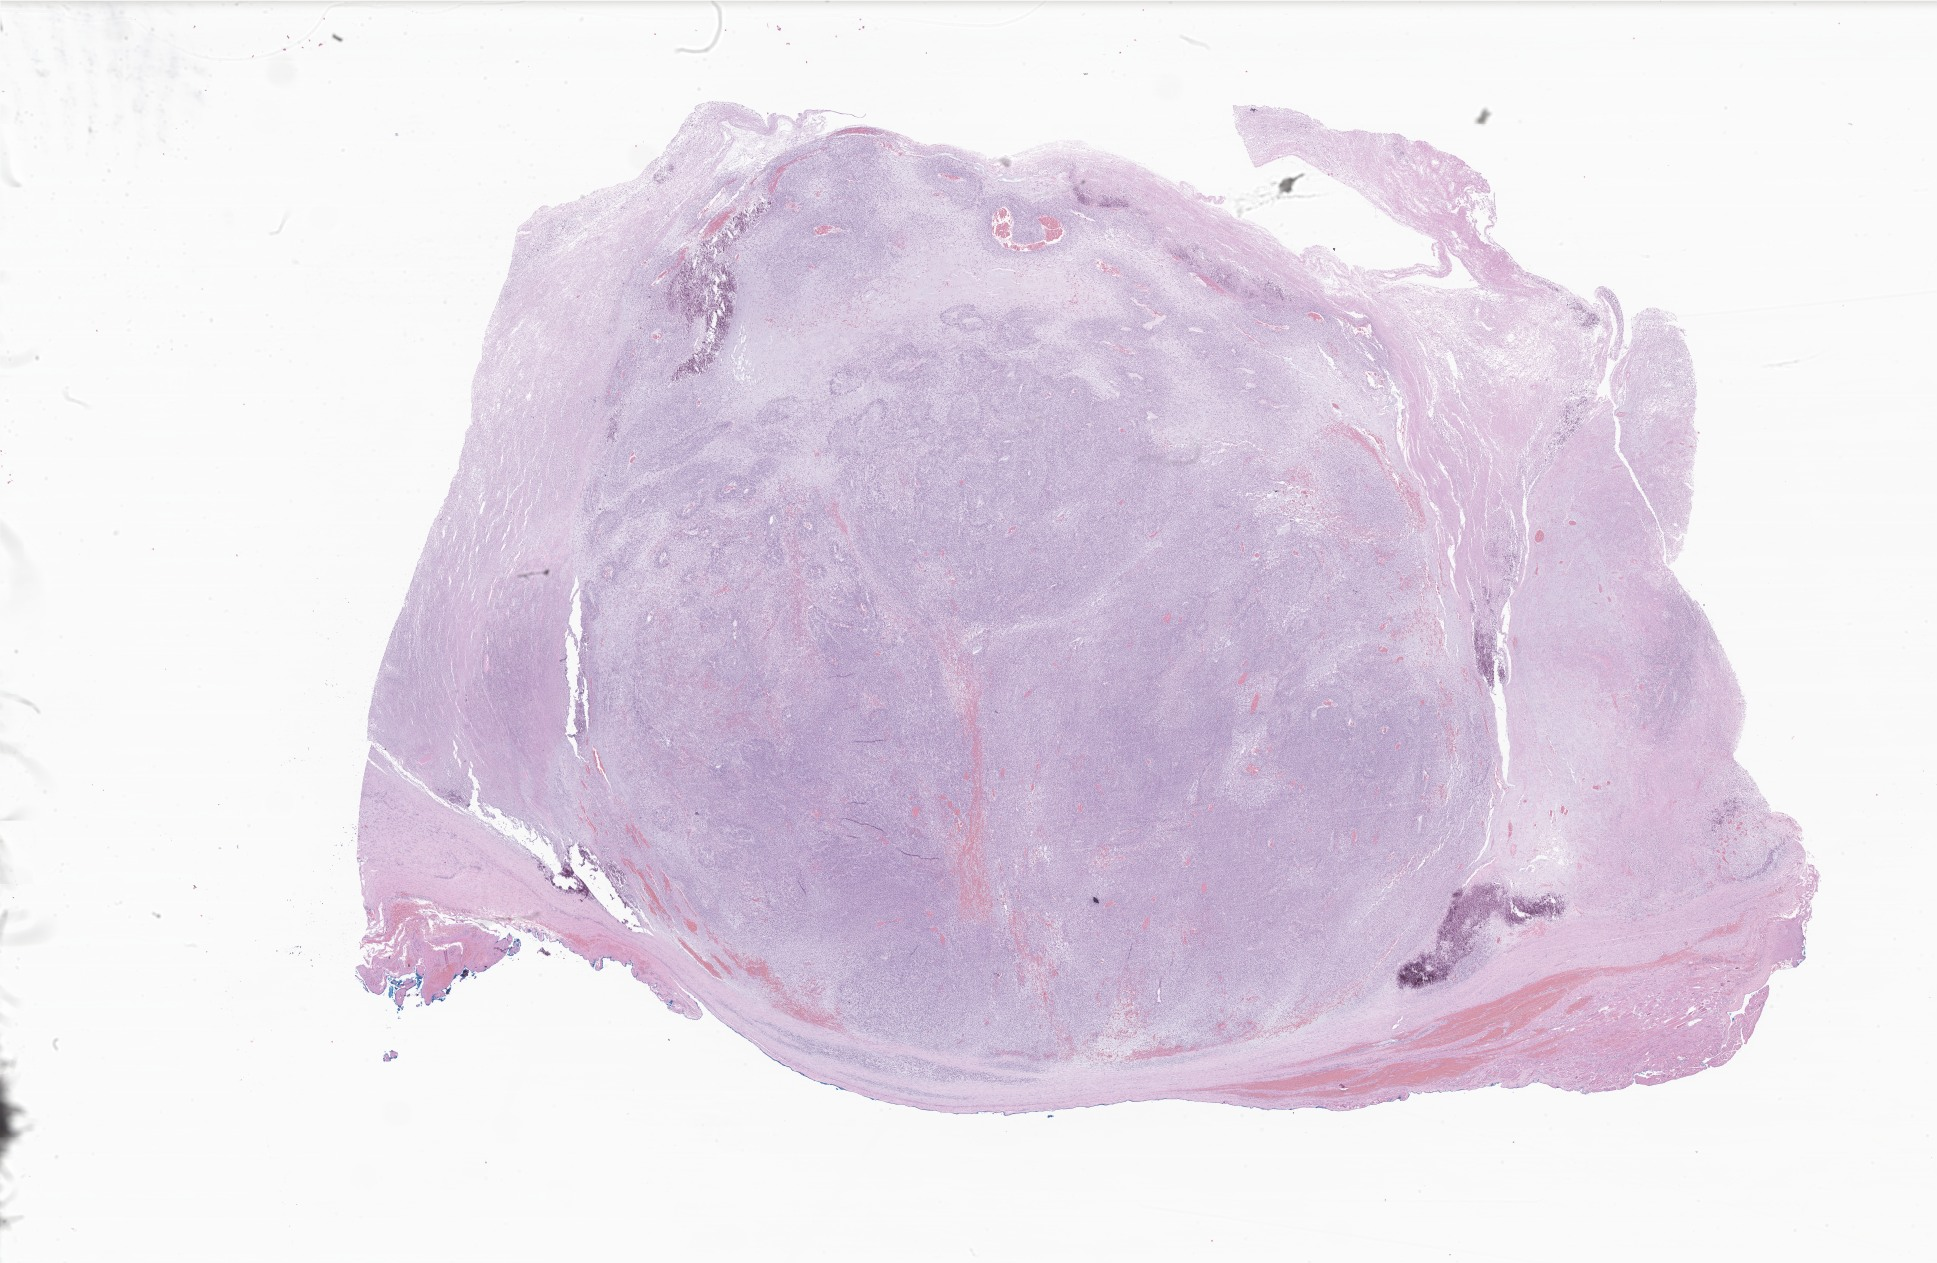
H&E whole-slide image of tumor tissue from the soft tissue, low-resolution overview of the scanned area, about 32.7 x 21.3 mm. Formalin-fixed paraffin-embedded section. Patient male; age 50 days.
Diagnosis: Sarcoma, NOS.